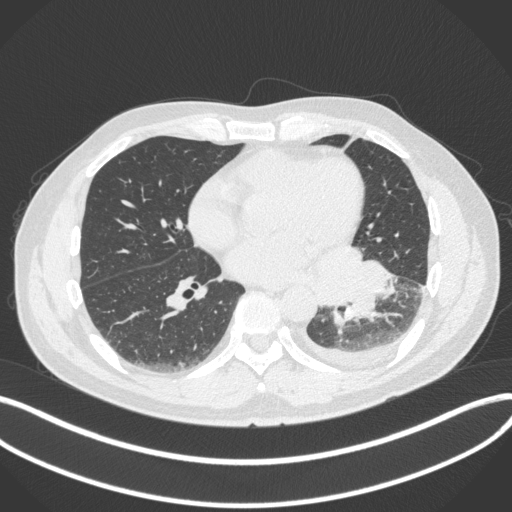
Chest CT, one axial slice; reconstruction kernel B31f; 120 kVp; lung window (W 1500 / L -600 HU); 1 mm slice thickness; 512 × 512 image matrix, field of view 400 × 400 mm. Patient: male, 58 years. From the clinical record (not read from this slice): clinical TNM (as recorded): T3 N1 M1b; histopathological grade: G3.
Structures marked on this image (rectangle marked by the reading radiologist):
- lung tumour (recorded histology: small cell carcinoma): bounding box <337,260,396,324> (left, top, right, bottom; pixels)